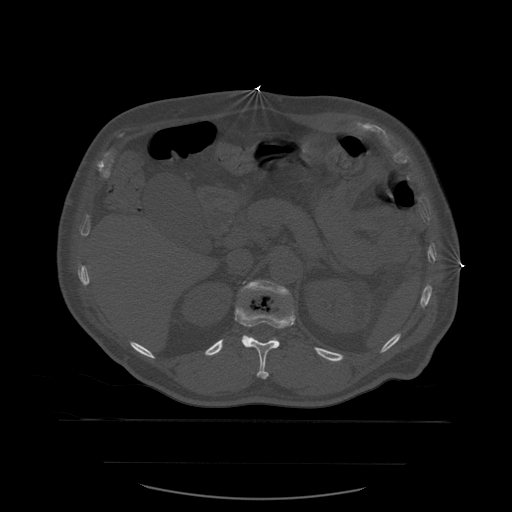
CT including the spine, one axial slice. Bone window (W 1800 / L 400 HU). 1.25 mm slice thickness. 512 × 512 image matrix, field of view 479 × 479 mm. Patient age 71 years. Case-level facts recorded for this patient, not image findings: primary cancer: lung; vertebrae with lytic lesions (as recorded): T1, T2, L5, S1.
Annotated regions visible in this slice (semi-automatically segmented with operator editing):
- L1 vertebra: bounding box <242,281,295,340> (left, top, right, bottom; pixels)
- T12 vertebra: <235,306,296,380>